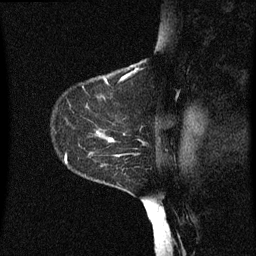
Breast MRI (dynamic contrast-enhanced), one sagittal slice; slice 47 of 60 in the series (ordered by position); dynamic contrast-enhanced series, image 2 of 3 at this slice position (ordered by acquisition); 1.5 T; TE 4.2 ms, TR 8 ms; 256 × 256 image matrix, field of view 200 × 200 mm. Patient: female, 55 years.
Annotated regions visible in this slice (semi-automatically segmented with operator editing):
- analysis volume of interest (the breast-tissue region the enhancement analysis was run in; not a lesion): bounding box (x1, y1, x2, y2) in pixels: (52, 124, 149, 183)
- tumour enhancement mask (voxels above the 70 % enhancement threshold inside the analysis volume of interest): (102, 134, 125, 167)